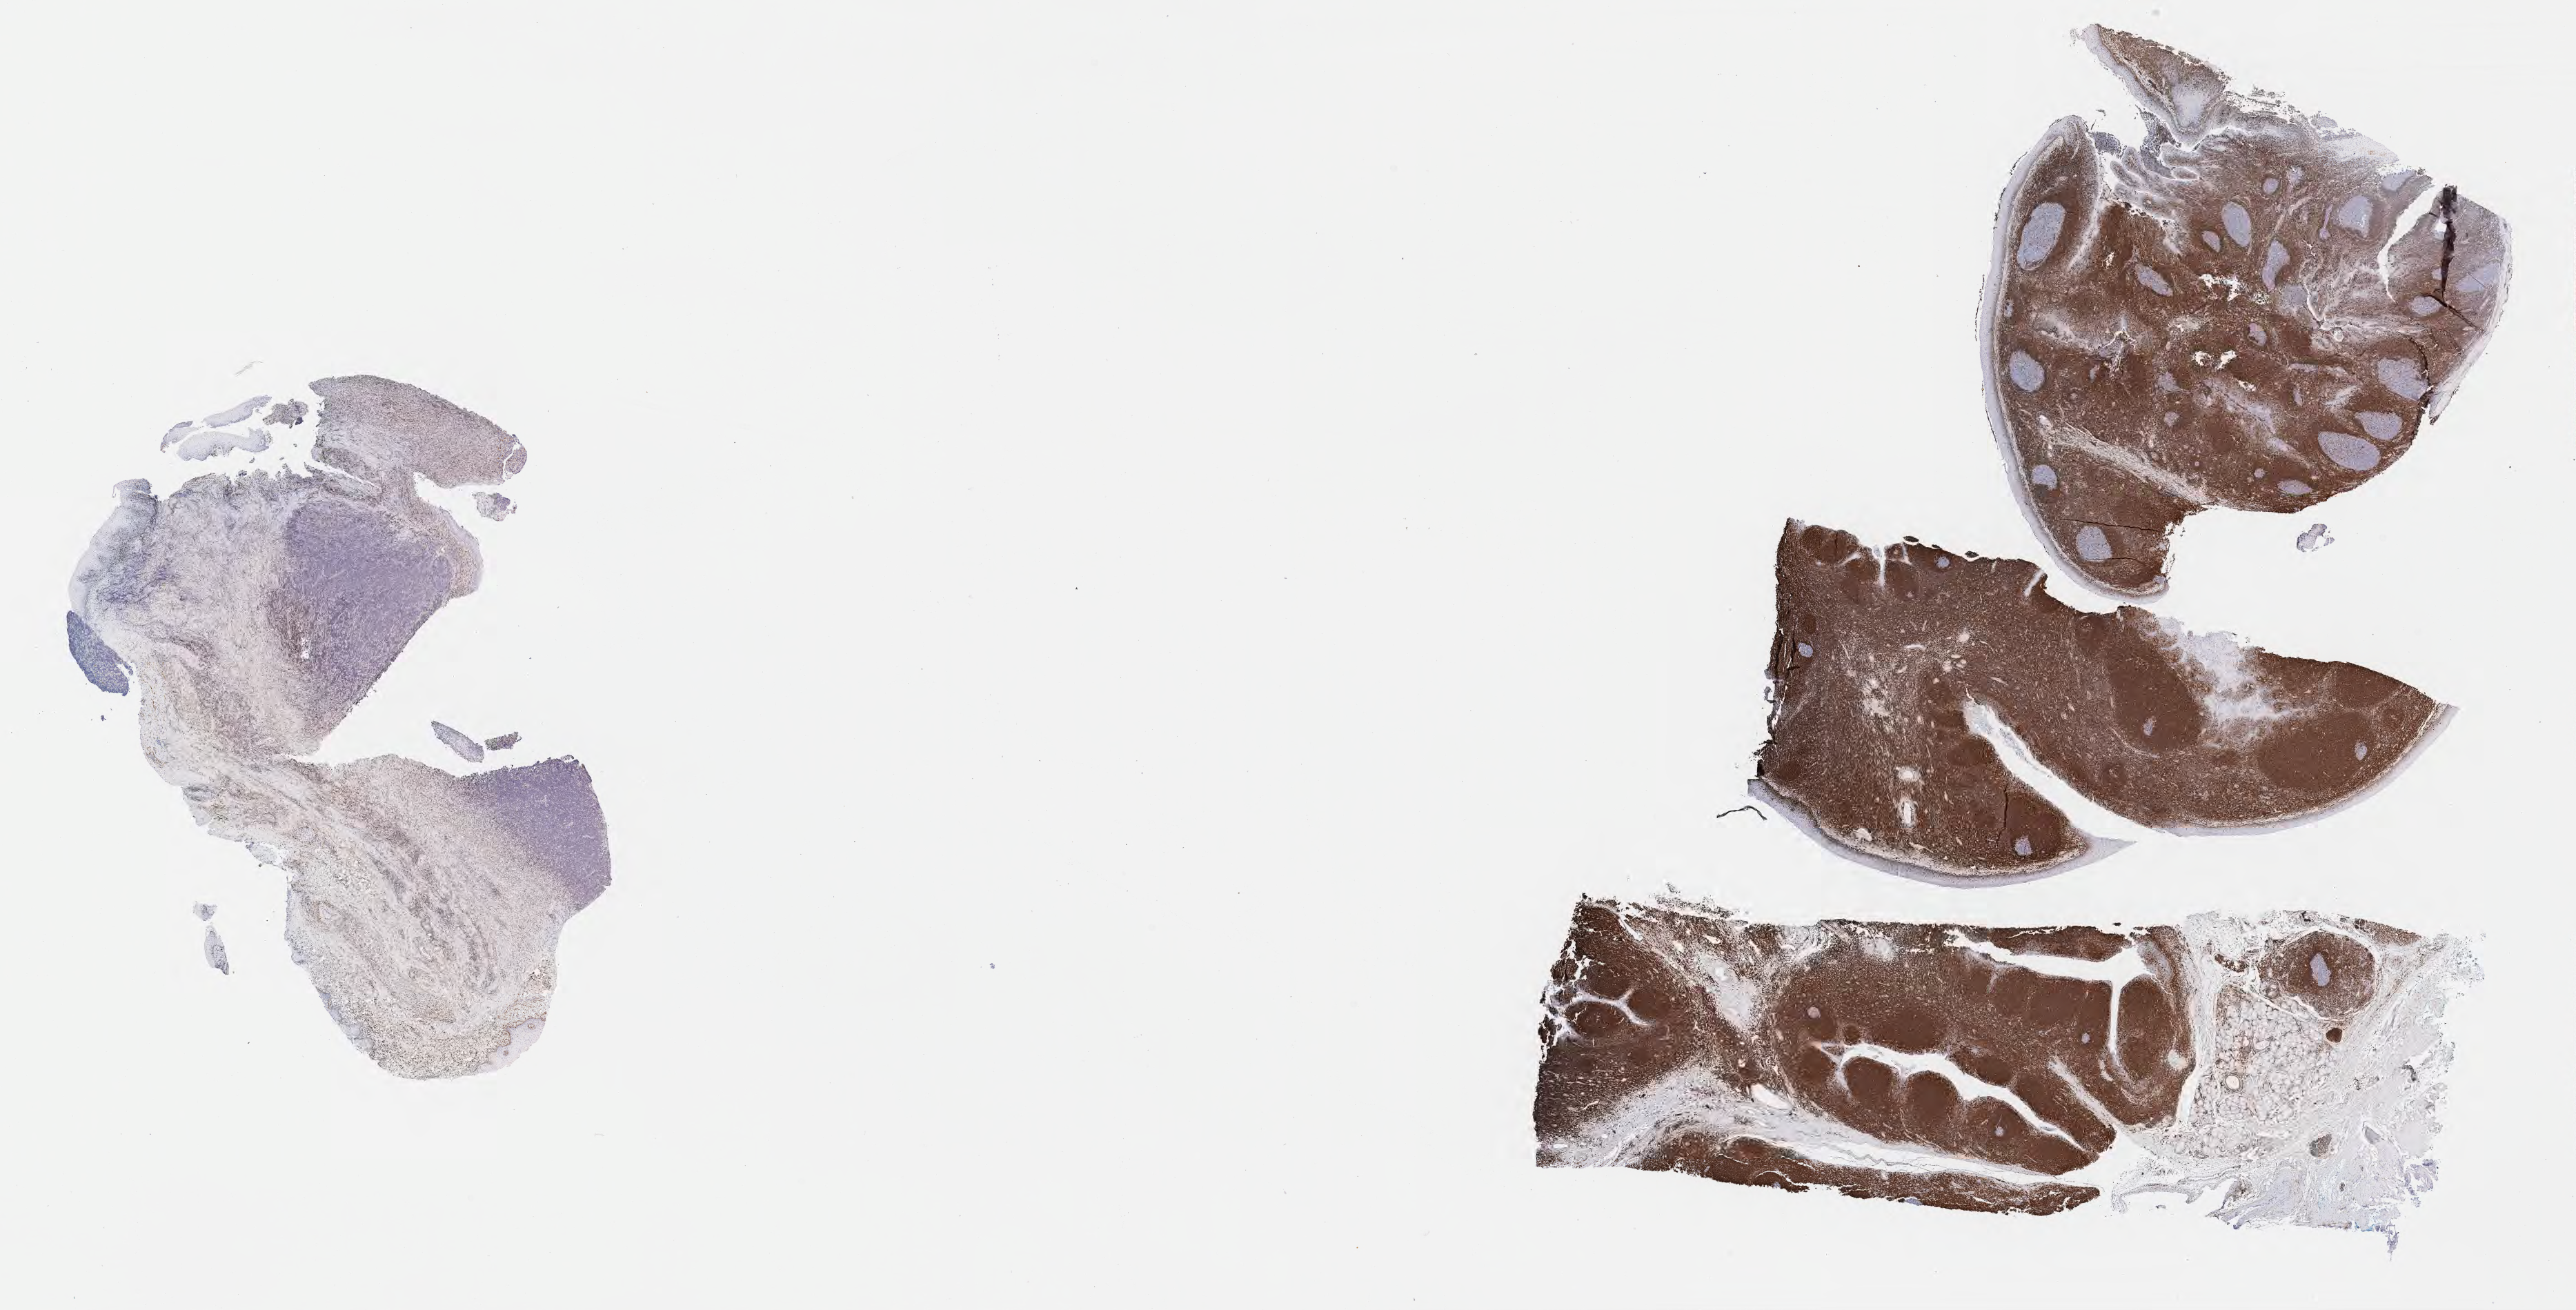
Immunohistochemistry (IHC) whole-slide image stained for BCL2, a low-resolution overview of the entire scanned area, about 30.2 x 15.4 mm, specimen: tumor tissue, site: cranium. Male patient, 10 years old.
Histologic diagnosis: Burkitt lymphoma, NOS.